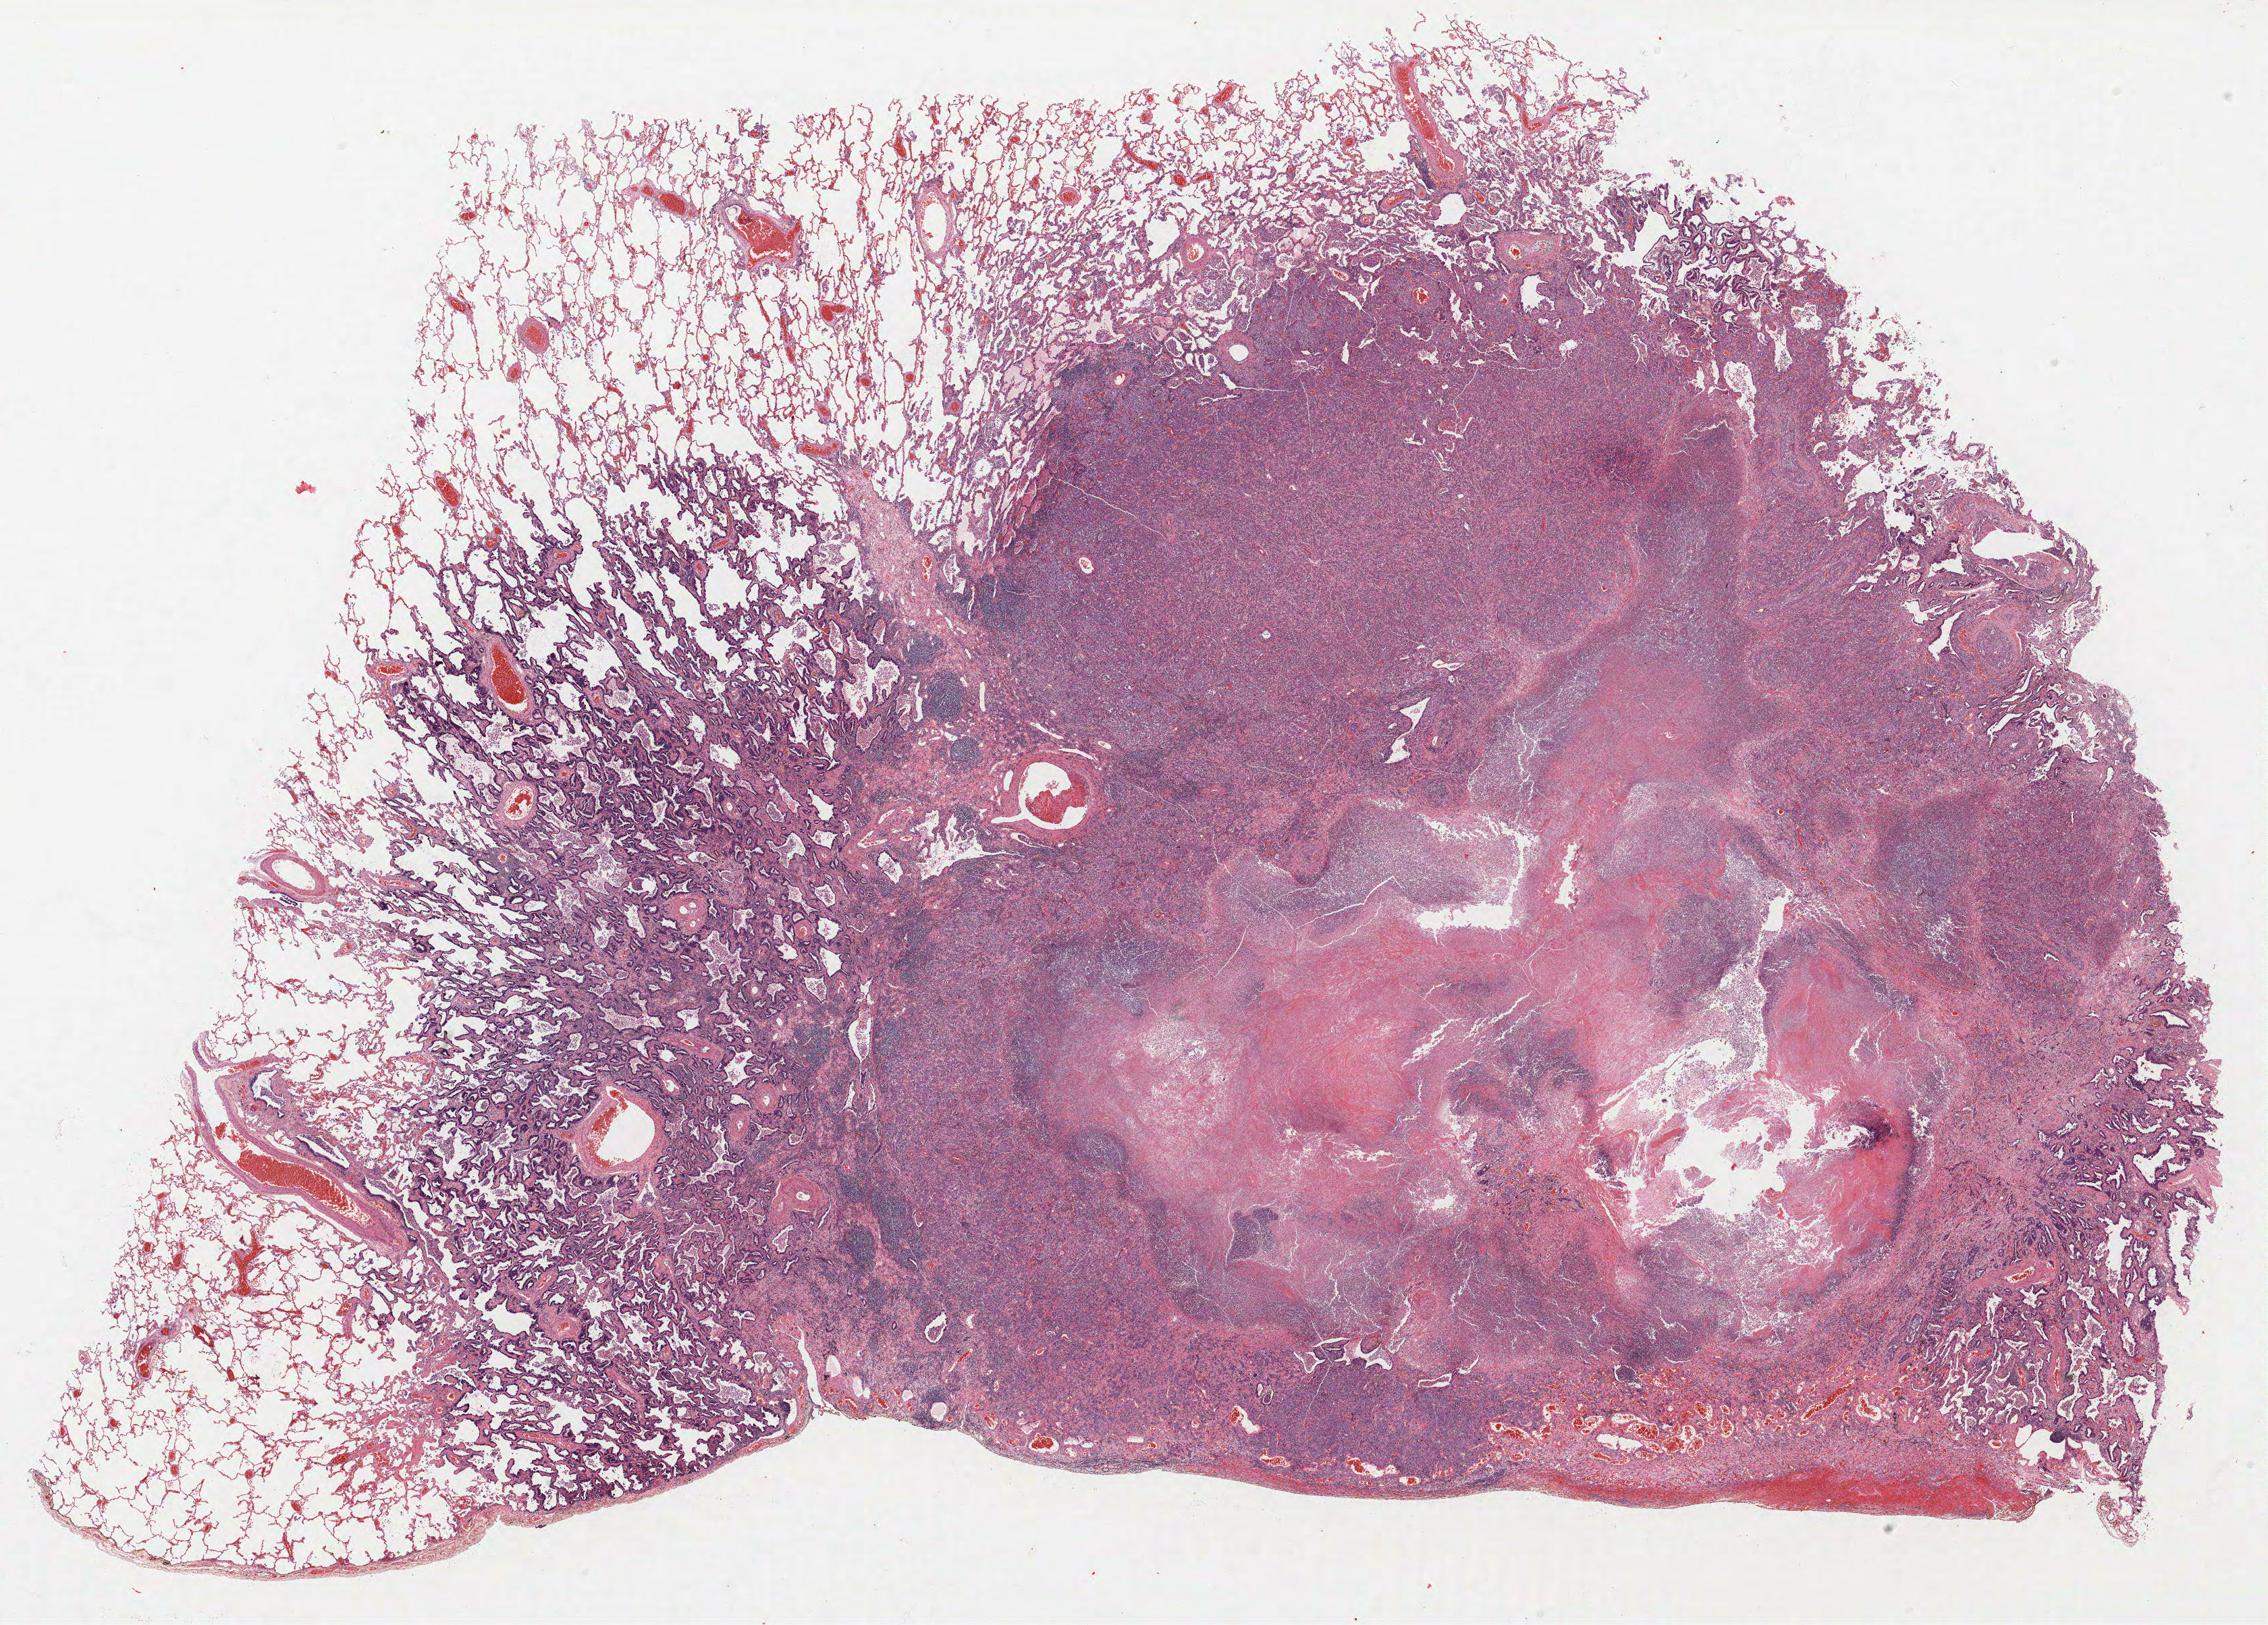
Whole-slide histology image, H&E — whole scanned area (about 26.9 x 19.3 mm) shown as a low-resolution overview. FFPE section. Lung tissue. Male patient, aged 60 at enrolment. Former smoker at enrolment. Grade: poorly differentiated (G3).
Stage (AJCC 6th edition): IIB. Participant's lung-cancer diagnosis: Adenocarcinoma, NOS. Tumour size (pathology): 35 mm. Primary tumour location (clinical record): right lower lobe.